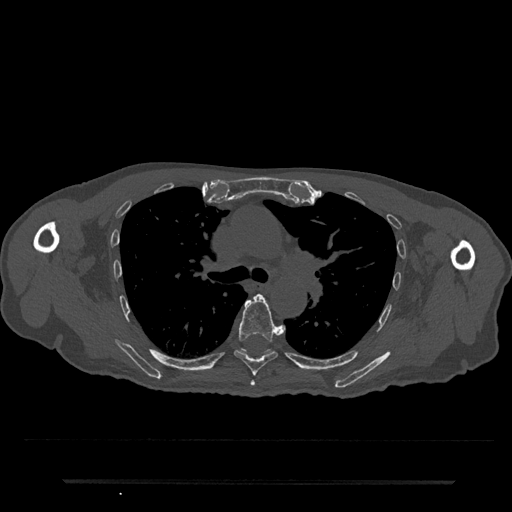
CT including the spine, one axial slice. Position 526 of 797 along the scan axis. Bone window (W 1800 / L 400 HU). 0.5 mm slice thickness. 512 × 512 image matrix, field of view 427 × 427 mm. Male patient, age 74 years. From the clinical record (not read from this slice): primary cancer: prostate.
Outlined on this slice (semi-automatically segmented with operator editing):
- T5 vertebra: bounding box [x1, y1, x2, y2] px = [250, 380, 255, 386]
- T6 vertebra: [234, 294, 285, 376]
- T7 vertebra: [241, 349, 246, 352]